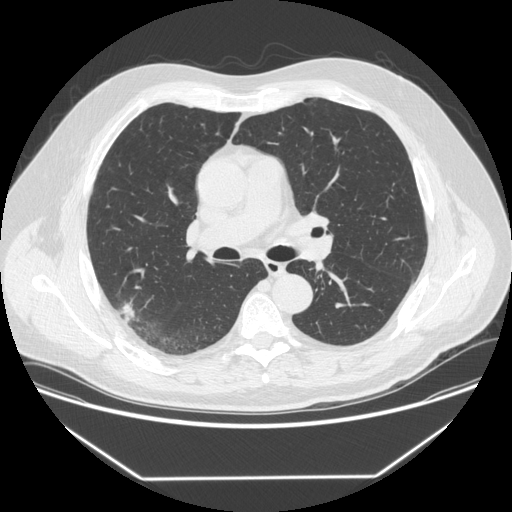
Low-dose screening chest CT, one axial slice. Slice 215 of 342 in the series (ordered by position). 120 kVp. Lung window (W 1500 / L -600 HU). 512 × 512 image matrix, field of view 410 × 410 mm.
Structures marked on this image (expert manual segmentation):
- lesion 1 (tumor, upper lobe of right lung): box from (x=119, y=303) to (x=135, y=324) px